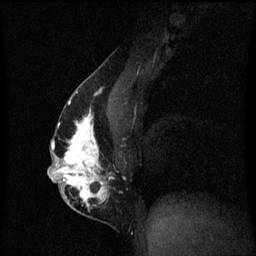
Breast MRI (dynamic contrast-enhanced), one sagittal slice; position 31 of 60 along the scan axis; dynamic contrast-enhanced series, image 2 of 3 at this slice position (ordered by acquisition); 1.5 T; TE 4.2 ms, TR 8.4 ms; 256 × 256 image matrix, field of view 200 × 200 mm. Female patient, age 40 years.
Outlined on this slice (semi-automatically segmented with operator editing):
- analysis volume of interest (the breast-tissue region the enhancement analysis was run in; not a lesion): bounding box <49,84,121,211> (left, top, right, bottom; pixels)
- tumour enhancement mask (voxels above the 70 % enhancement threshold inside the analysis volume of interest): <49,88,113,209>